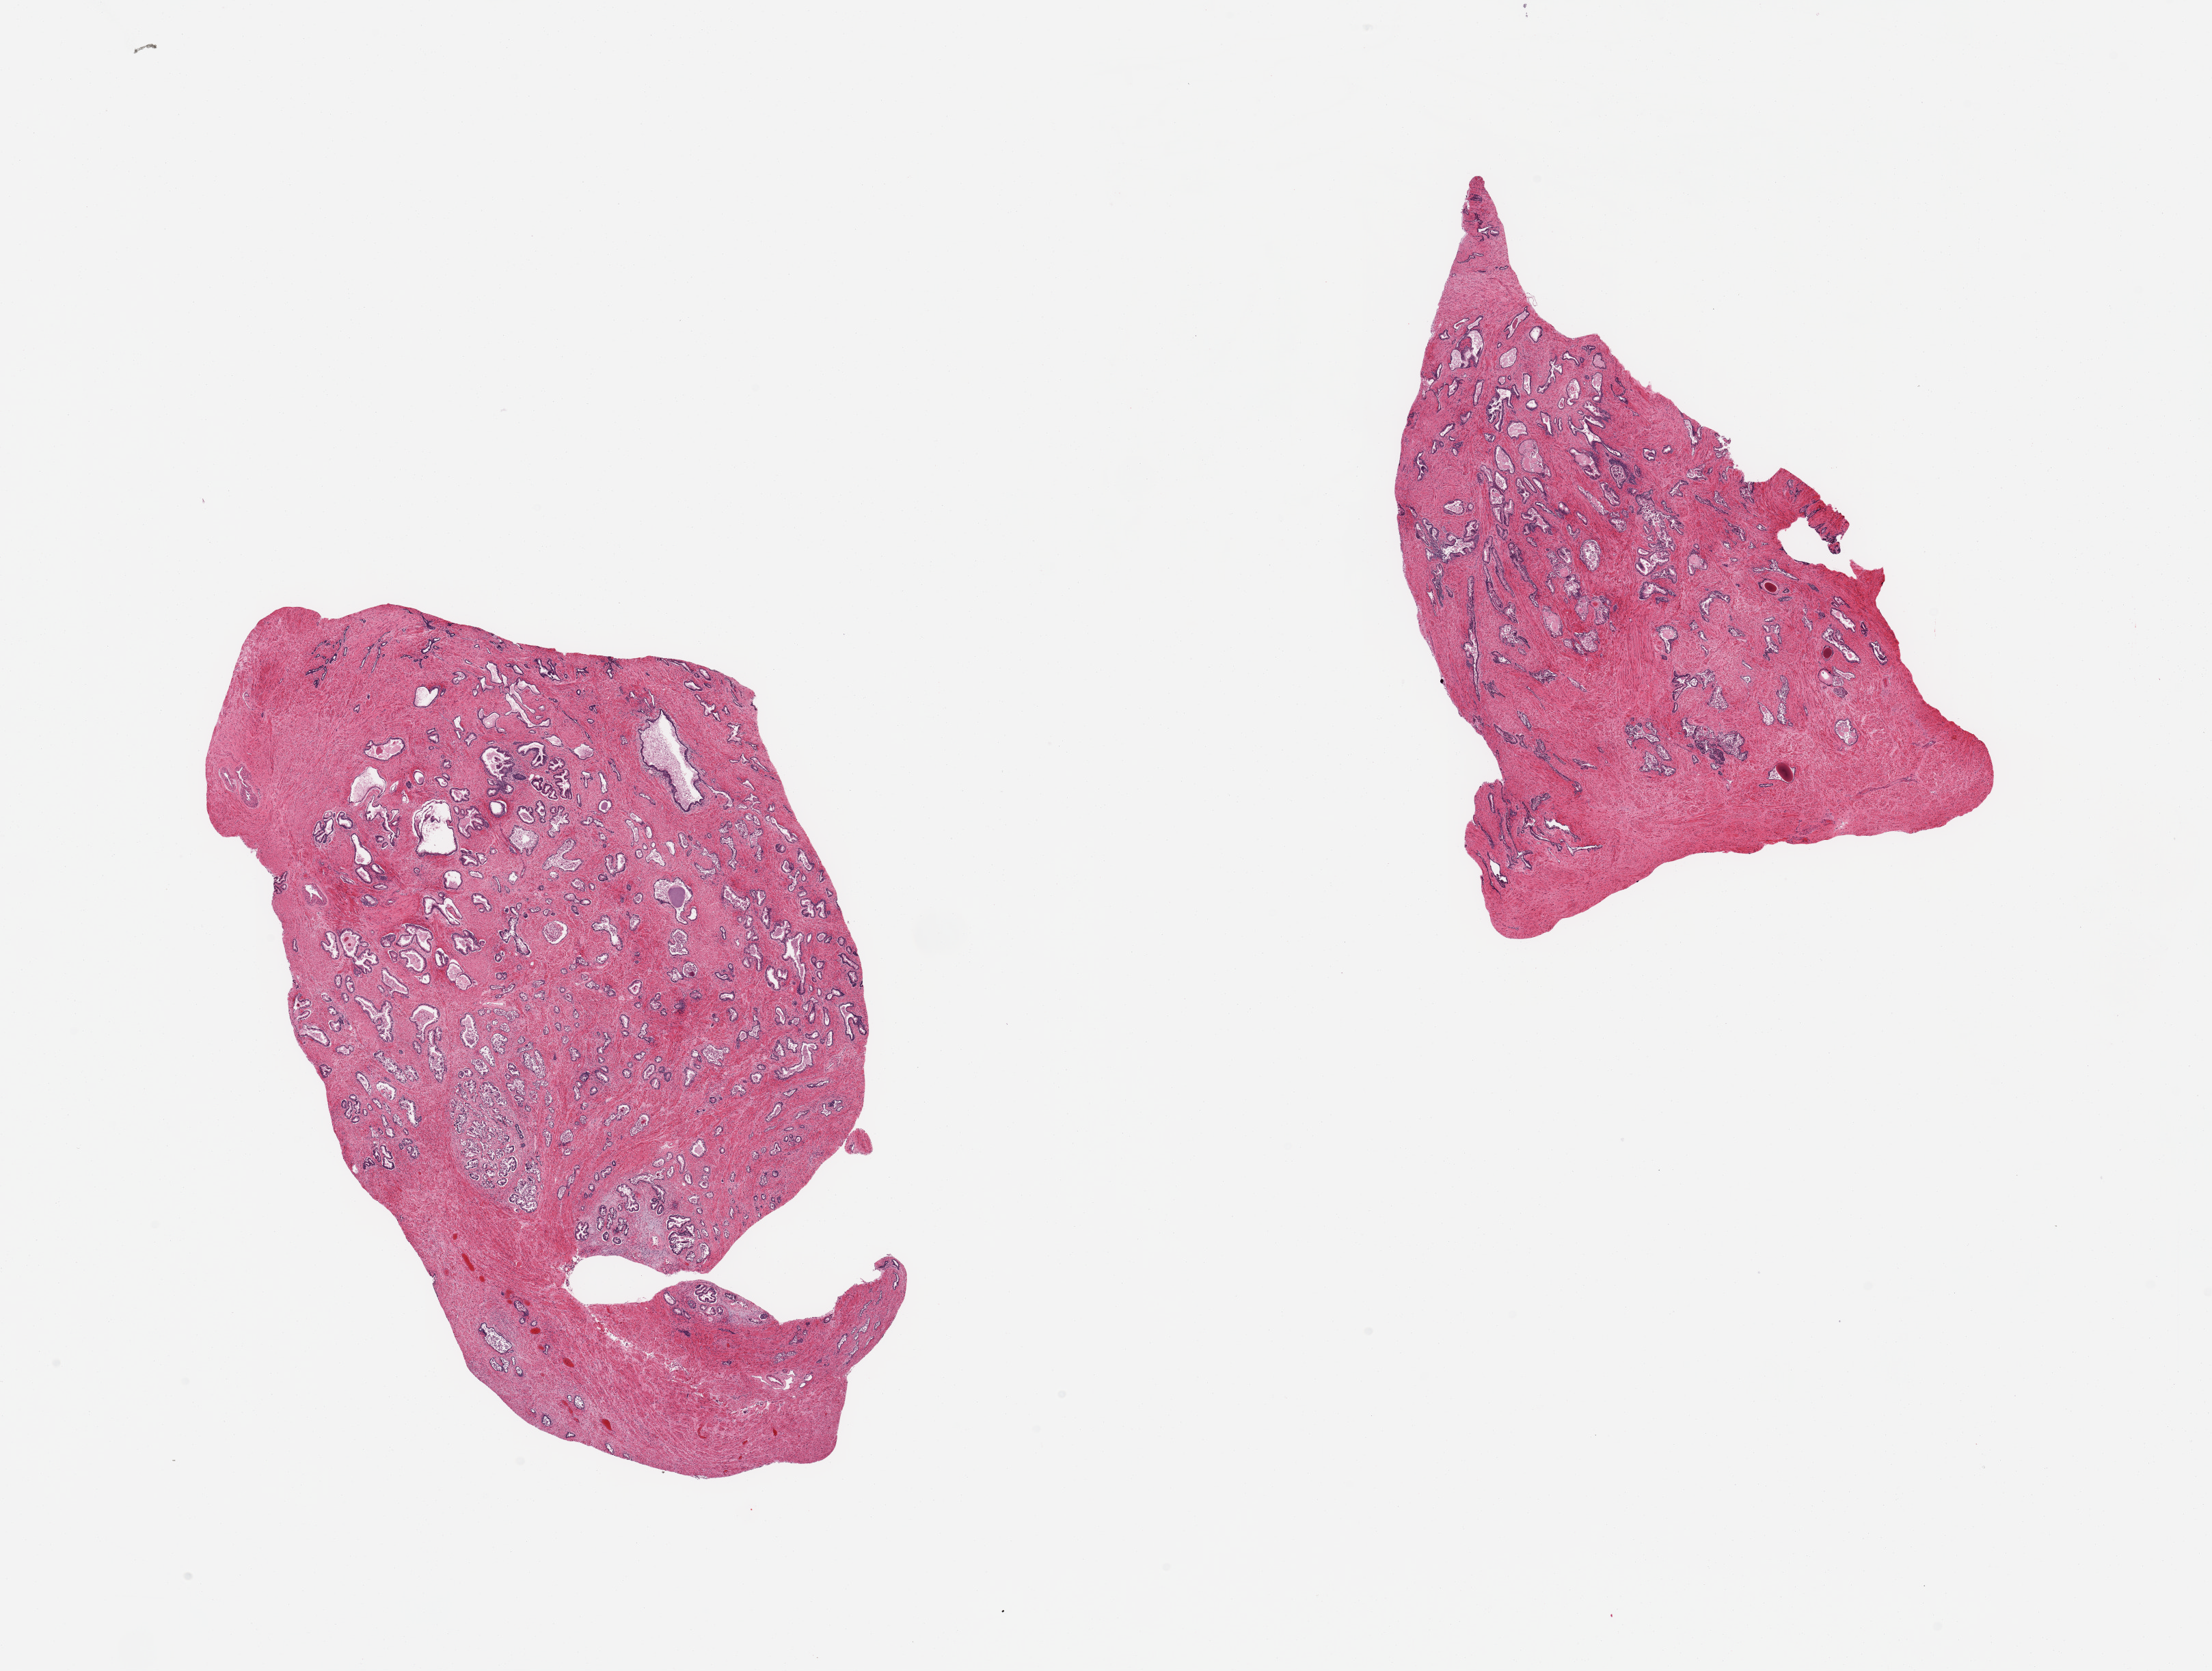
Digitized H&E-stained section, low-resolution overview of the scanned area, about 25.6 x 19.3 mm, PAXgene-fixed paraffin-embedded (PFPE) section, target tissue: prostate, tissue donor sample. Donor sex: male.
Pathologist's review note for this sample: 2 pieces; glands moderately autolyzed, stroma intact.